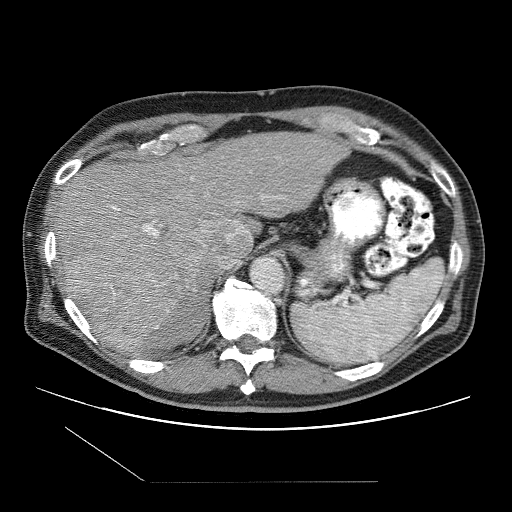
Contrast-enhanced abdominal CT (liver protocol), one axial slice; position 74 of 109 along the scan axis; one of 2 acquisitions stored at this slice position; soft-tissue window (W 400 / L 40 HU); 2.5 mm slice thickness; 512 × 512 image matrix. From the clinical record (not read from this slice): diagnosis: hepatocellular carcinoma (patient treated with transarterial chemoembolisation; whether this scan precedes or follows treatment is not stated here); TNM stage (as recorded): Stage-IIIB; Child-Pugh class: A; tumour differentiation: well differentiated.
Outlined on this slice (semi-automatically segmented with operator editing):
- liver parenchyma outside the tumour (the mass and vessels are separate outlines, so this box may not span the whole liver): bounding box (x1, y1, x2, y2) in pixels: (56, 132, 346, 354)
- mass: (68, 246, 197, 350)
- liver vessels: (112, 141, 266, 237)